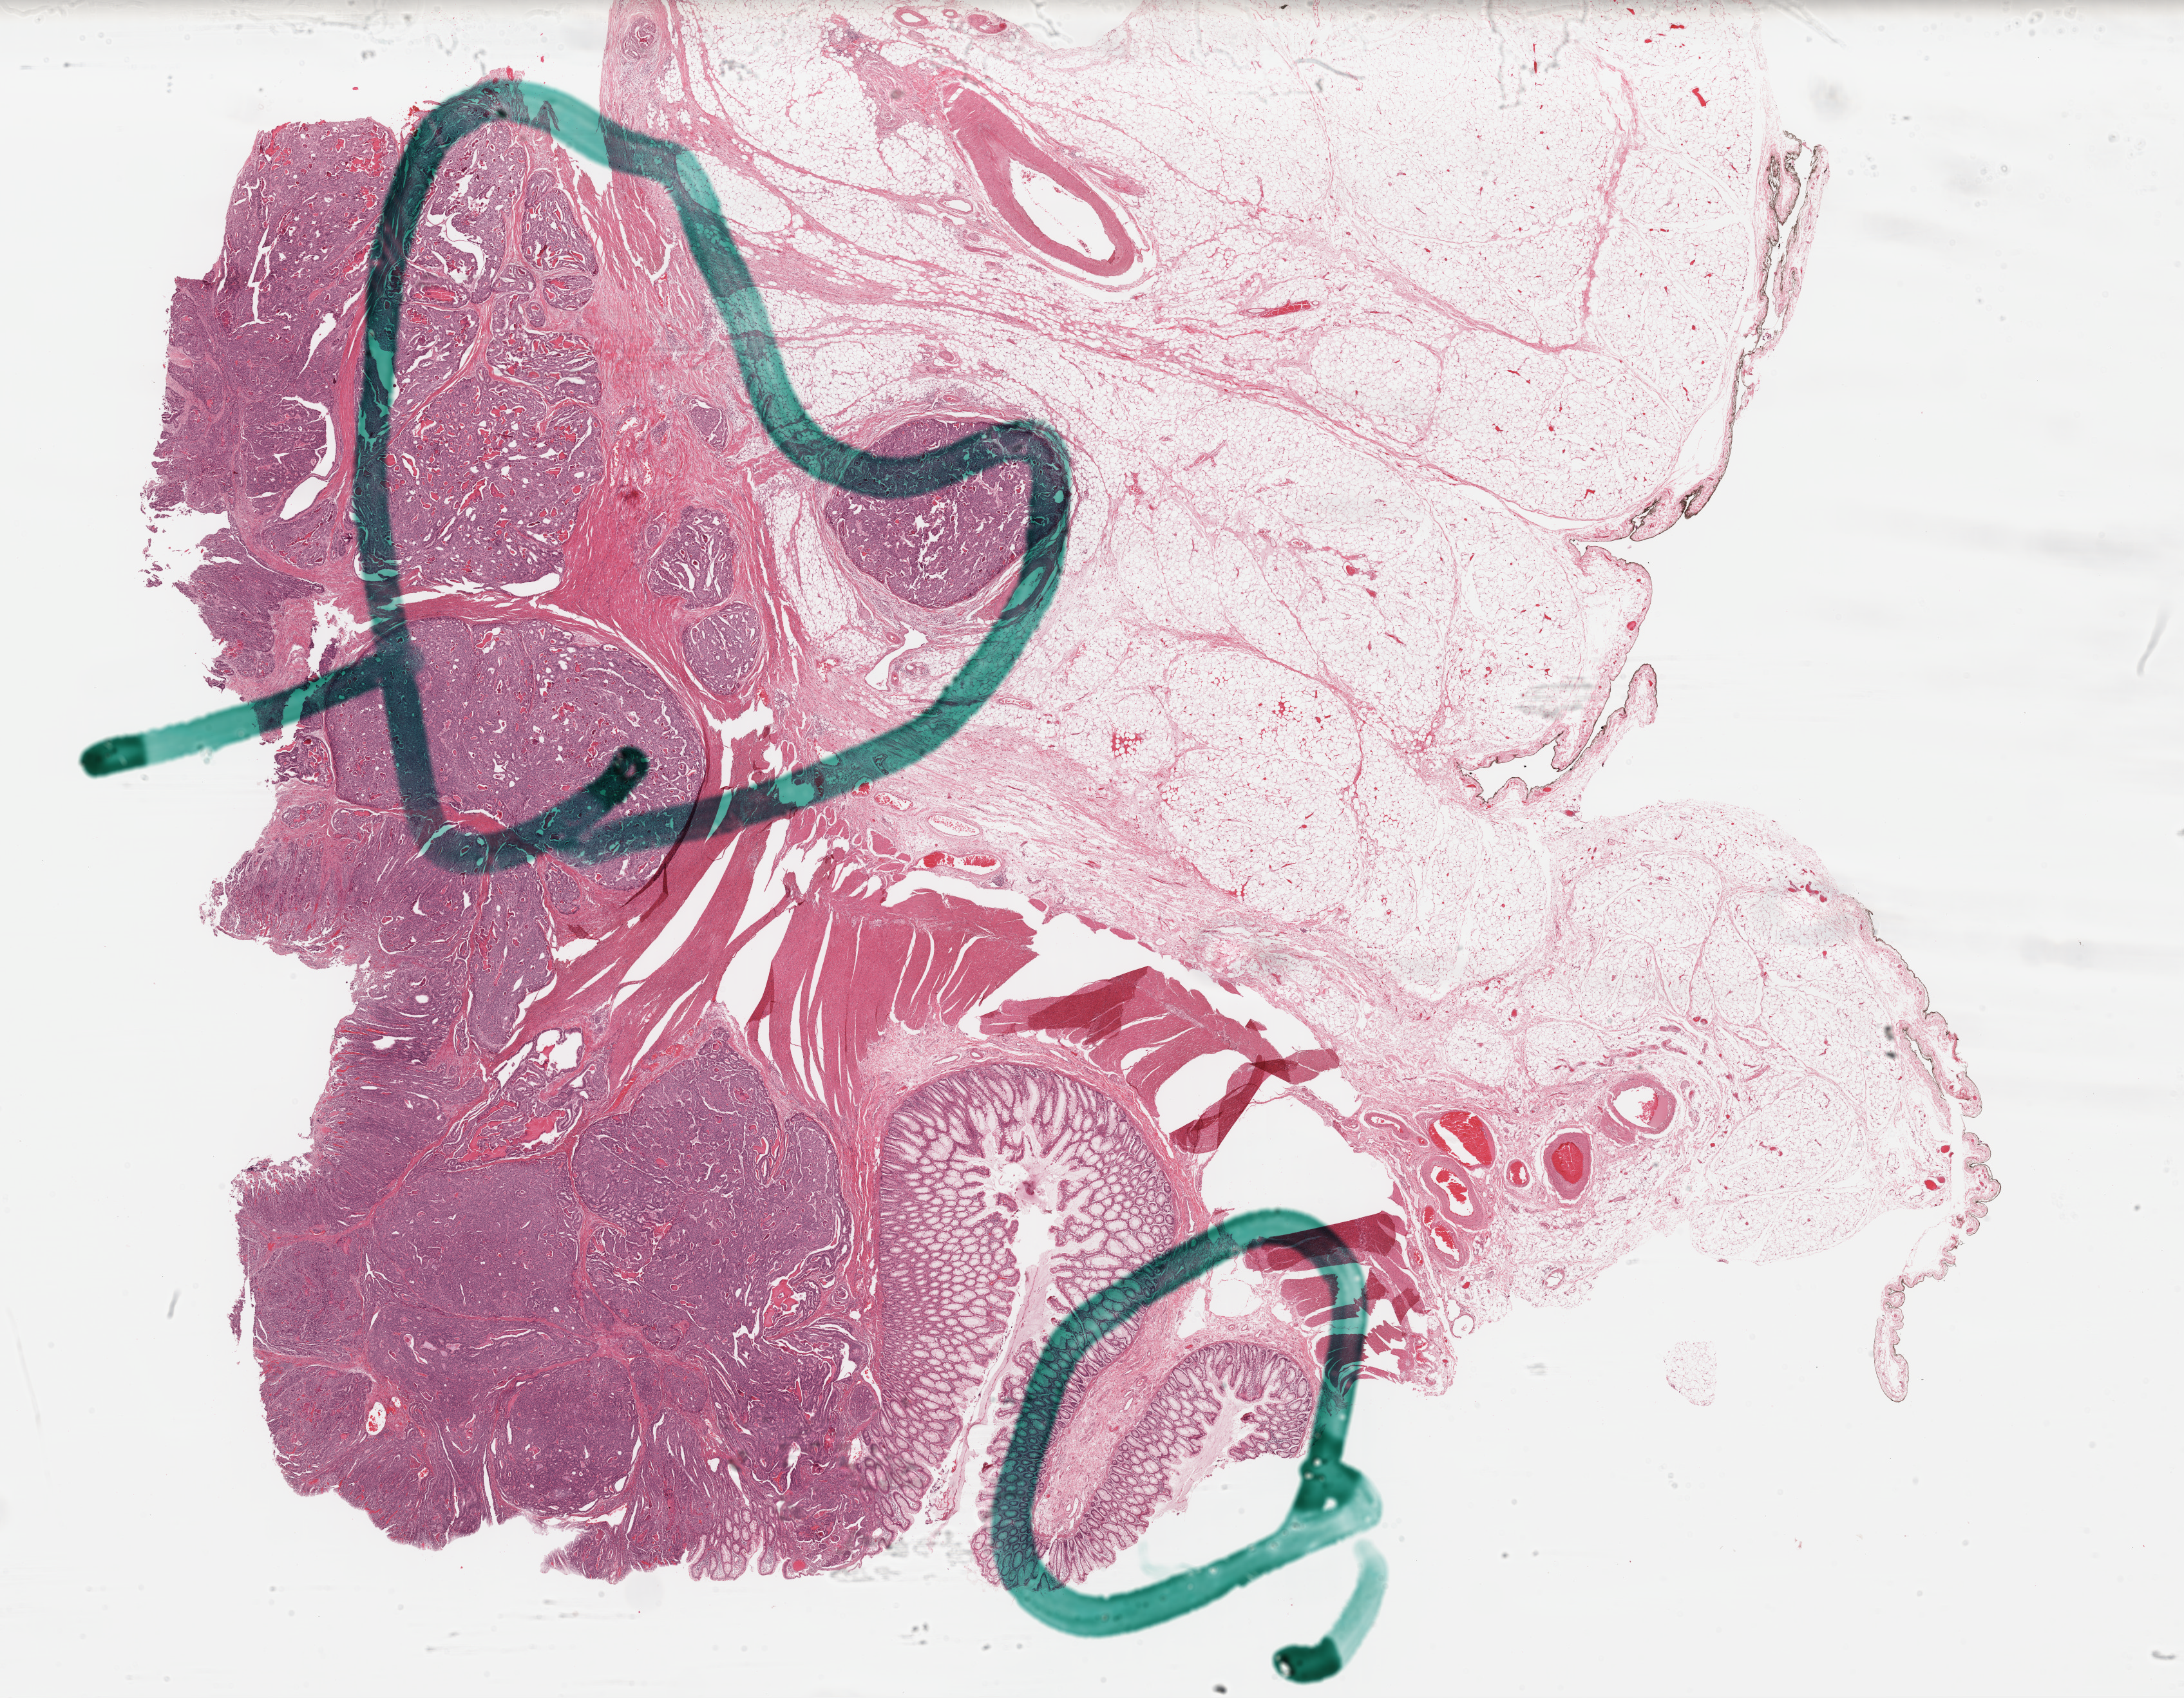
Whole-slide histology image, H&E-stained, whole scanned area (about 26.8 x 20.8 mm, slide scanned at 40x) shown as a low-resolution overview; formalin-fixed paraffin-embedded (FFPE) diagnostic section; rectum, primary tumour sample. Female, age 77 years at initial diagnosis.
- diagnosis: Adenocarcinoma, NOS
- AJCC pathologic stage: IIIB